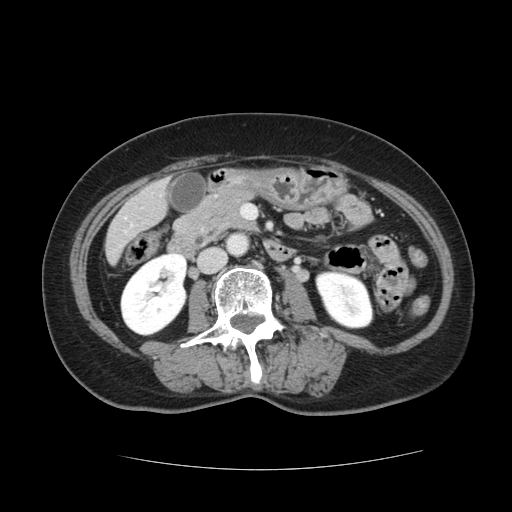
Contrast-enhanced abdominal CT, one axial slice. Position 28 of 128 along the scan axis. Intravenous contrast given. Soft-tissue window (W 400 / L 40 HU). 2.5 mm slice thickness. 512 × 512 image matrix, field of view 366 × 366 mm. Female patient, age 67 years. From the clinical record (not read from this slice): diagnosis: colorectal cancer liver metastases, imaged before liver resection; multiple liver metastases: yes; largest metastasis: 3 cm; disease in both lobes: yes.
Outlined on this slice (manually delineated by an expert):
- liver: bounding box [x1, y1, x2, y2] px = [106, 182, 167, 260]
- planned liver remnant (the part of the liver to remain after resection): [106, 211, 139, 260]